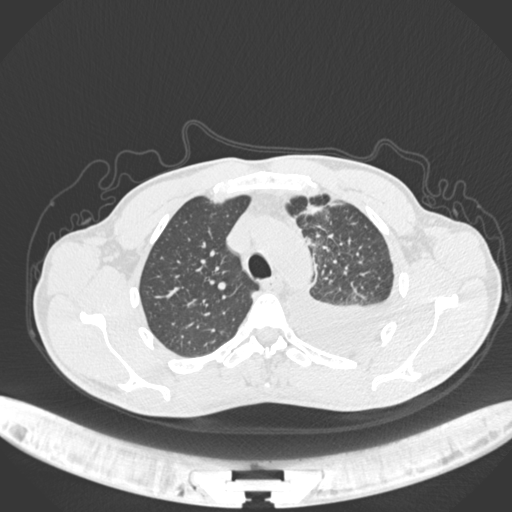
Chest CT, one axial slice. Slice 170 of 244 in the series (ordered by position). Reconstruction kernel B30f. 120 kVp. Lung window (W 1500 / L -600 HU). 1 mm slice thickness. 512 × 512 image matrix. Patient: male, 49 years. Case-level facts recorded for this patient, not image findings: clinical TNM (as recorded): T1c N1 M1.
Outlined on this slice (bounding box drawn by a radiologist):
- lung tumour (recorded histology: adenocarcinoma): bounding box [x1, y1, x2, y2] px = [297, 200, 332, 222]